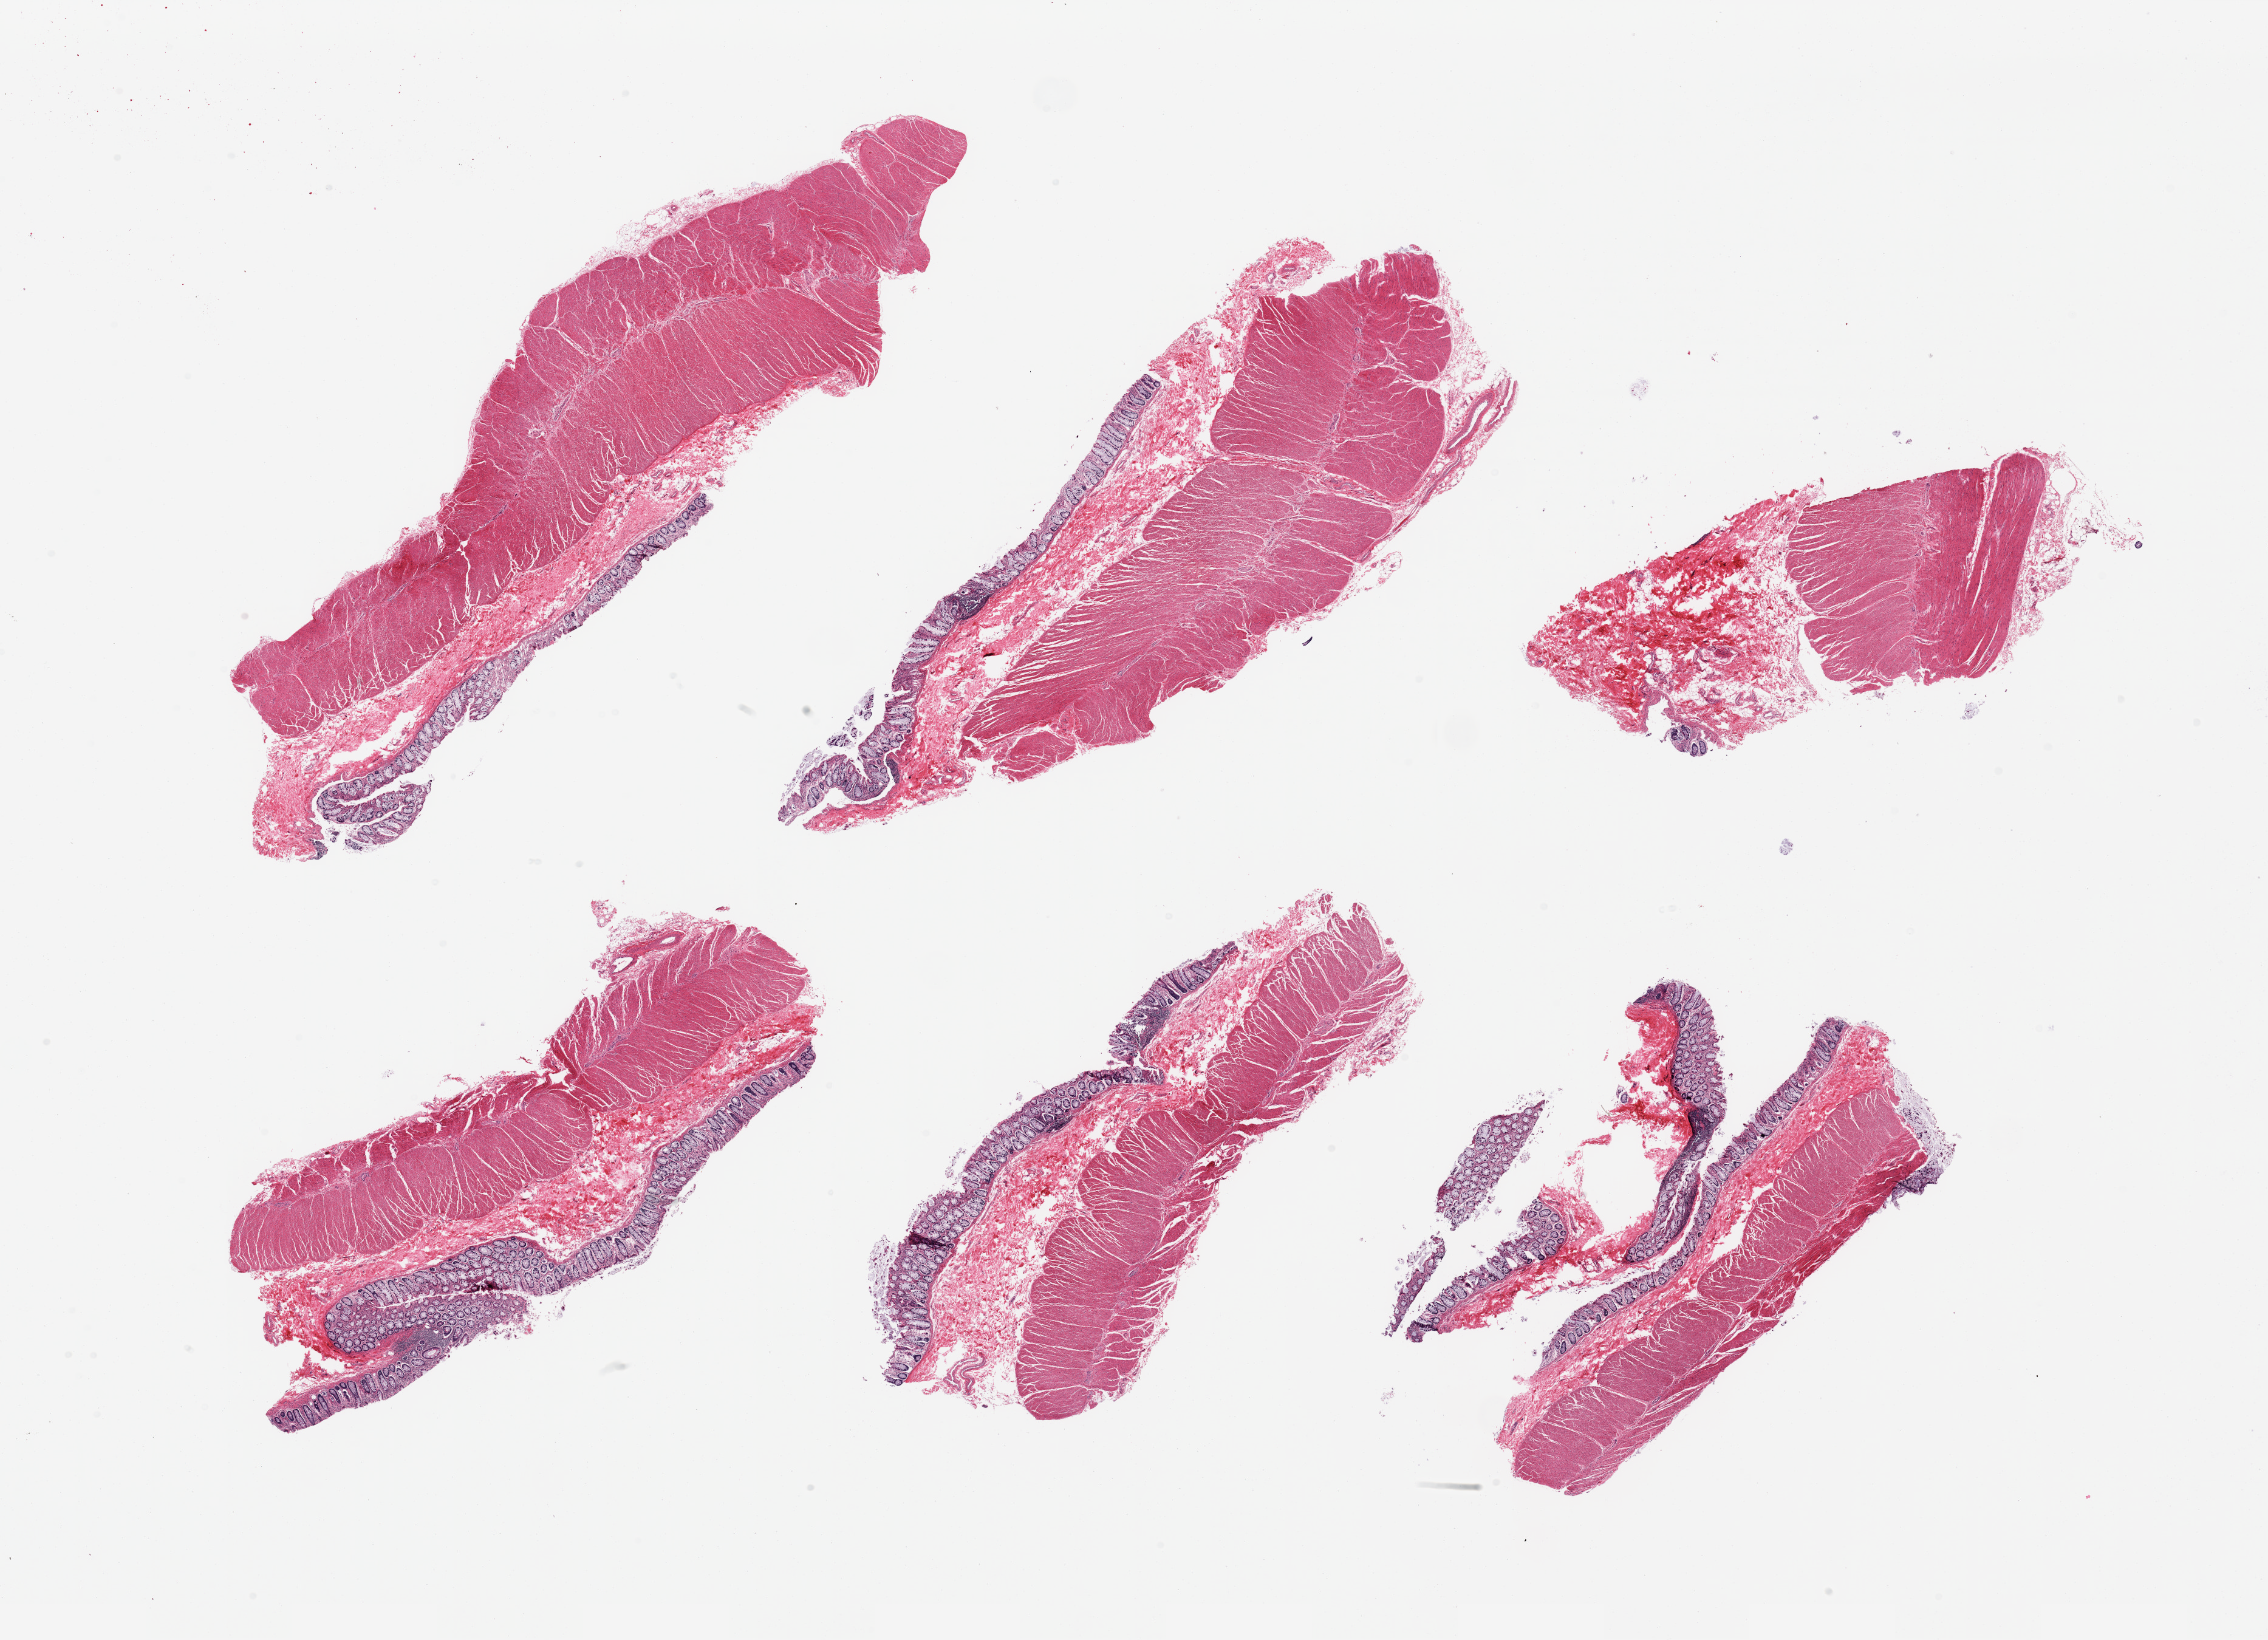
Hematoxylin and eosin (H&E) whole-slide image, brightfield, a low-resolution overview of the entire scanned area, about 29.5 x 21.4 mm (acquisition: 20x scan). Male donor.
Specimen: PAXgene-fixed paraffin-embedded (PFPE) section; target tissue: sigmoid colon; donor tissue sample.